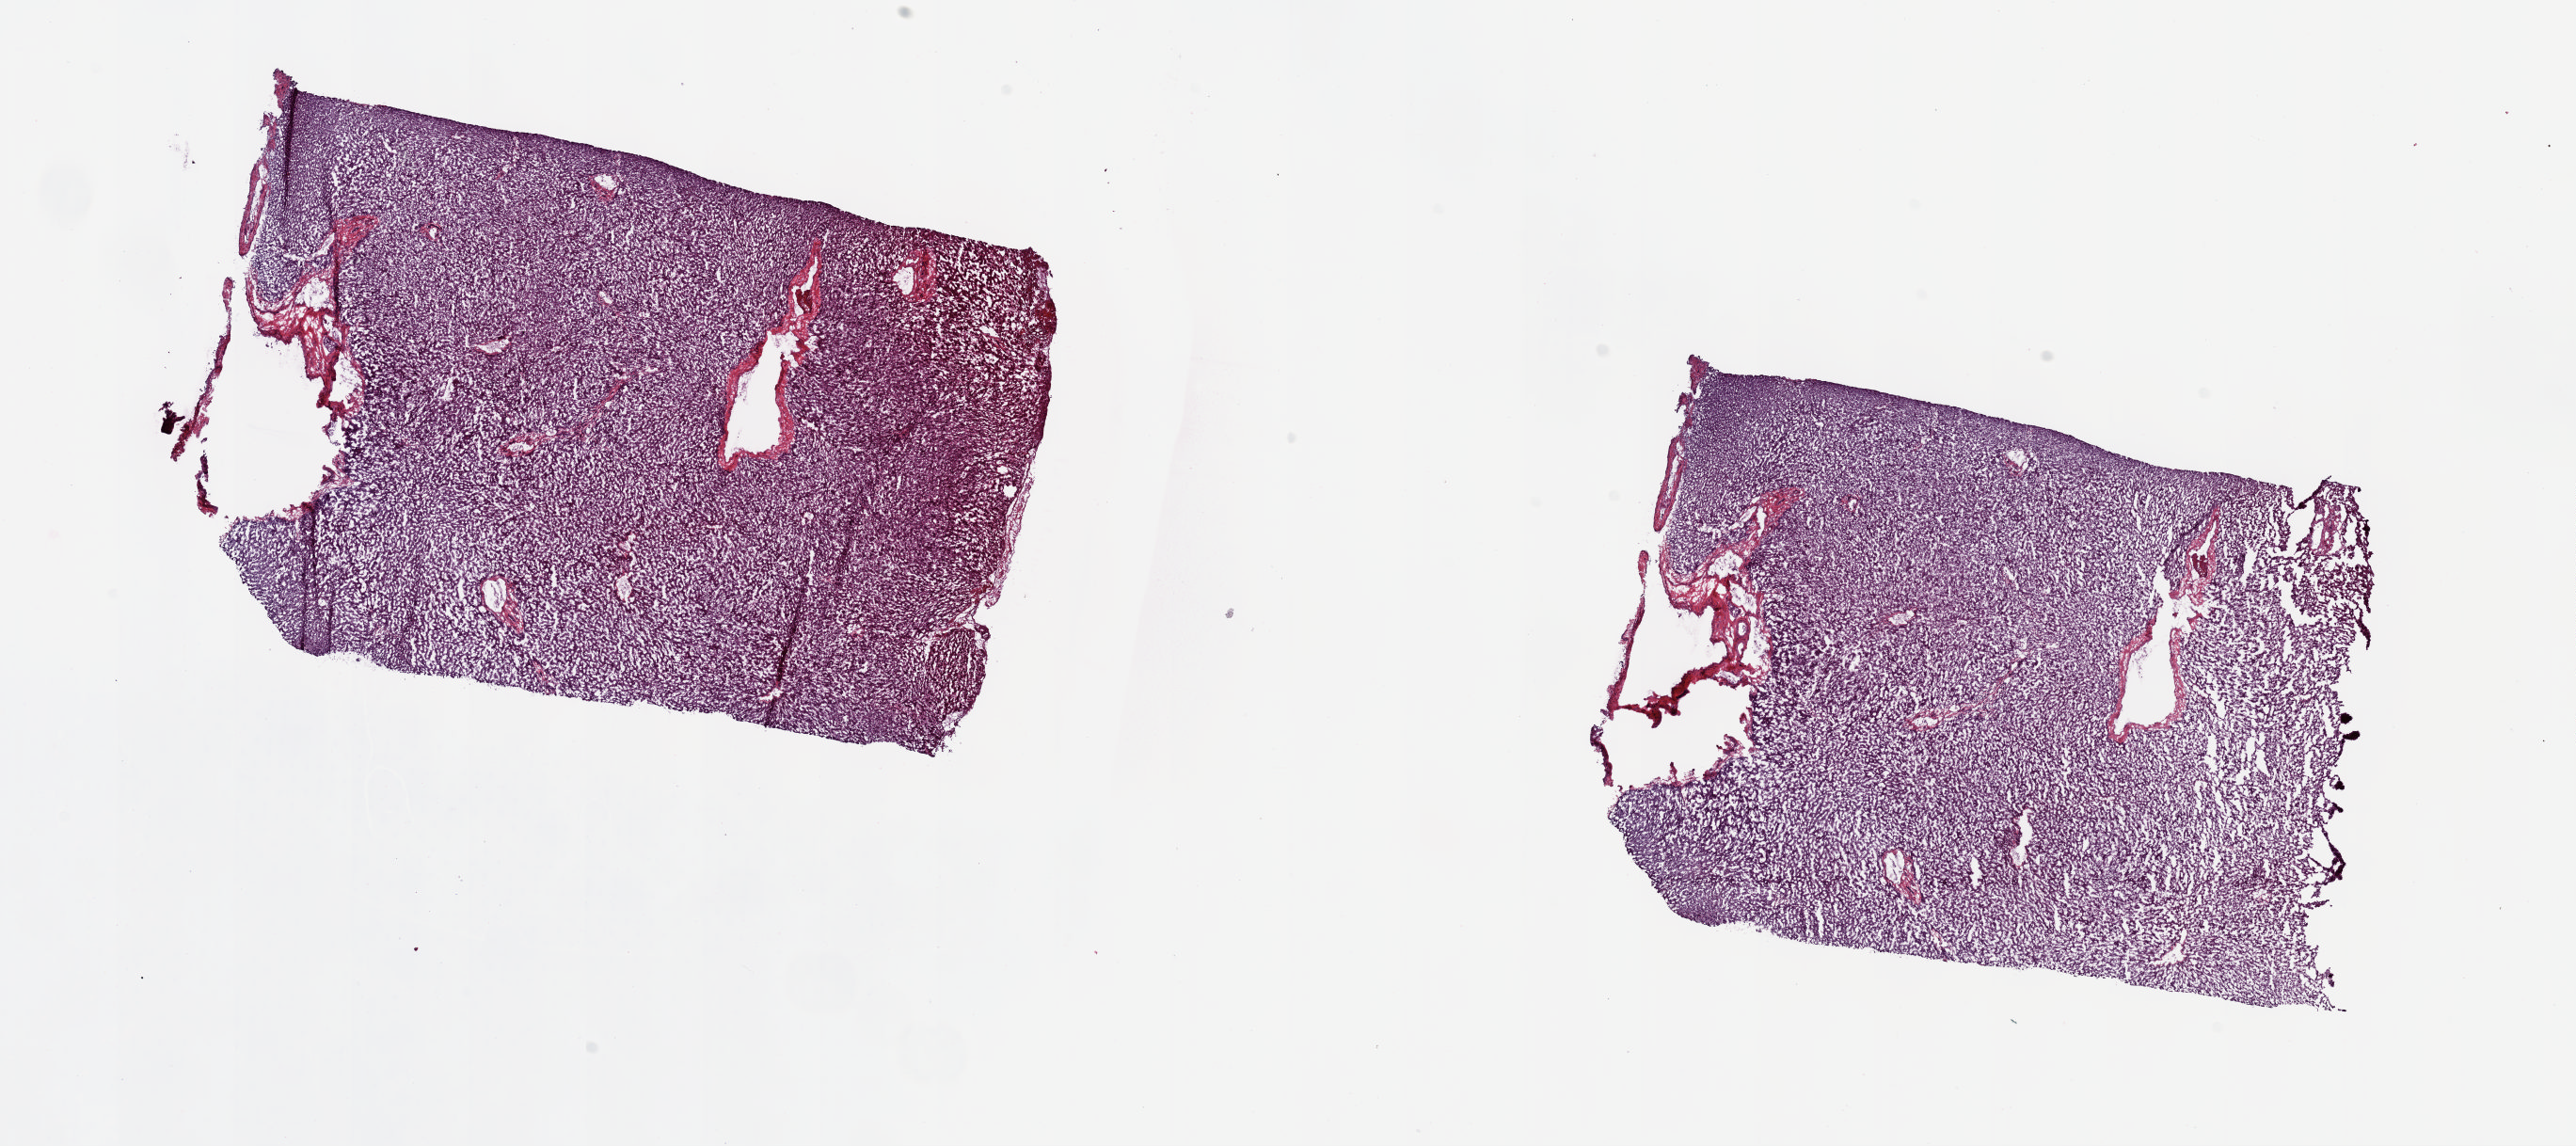
Whole-slide histology image, H&E-stained, whole scanned area (about 21.6 x 9.6 mm, slide scanned at 20x) shown as a low-resolution overview, frozen section from the top of the tissue portion, sample: solid tissue normal (non-tumour tissue), liver. Male, age 32 years at initial diagnosis. Pathologist review of this section (percent, as recorded): tumour cells 0%, tumour nuclei 0%, normal cells 100%, stromal cells 0%, necrosis 0%. Infiltration values recorded for this section: lymphocyte infiltration 2%, monocyte infiltration 0%, neutrophil infiltration 0%.
- this section: solid tissue normal (non-tumour) sample from the same patient
- patient diagnosis: Hepatocellular carcinoma, NOS